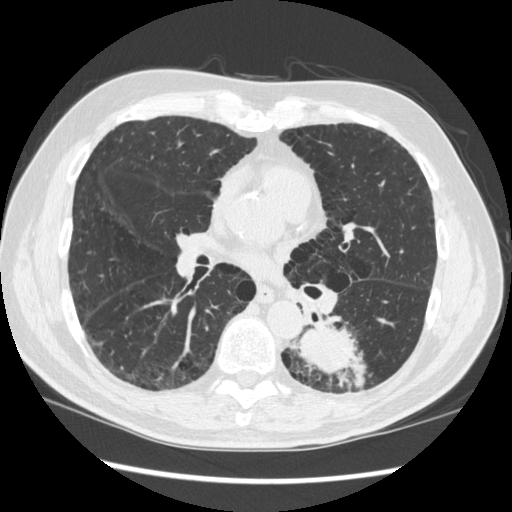
Chest CT (low-dose screening protocol), one axial image, first (baseline) screen, lung window (W 1500 / L -600 HU), 1.25 mm slice thickness, standard (soft-tissue) reconstruction kernel (STANDARD), 512 × 512 image matrix, field of view 360 × 360 mm. Male, age 72 years at enrolment.
• Expert reader's lesion annotation, bounding box (x1, y1, x2, y2) in pixels: (265, 305, 369, 398).
• The screening reader recorded 2 non-calcified nodules or masses ≥4 mm on this exam (left lower lobe, right middle lobe); which of them this box marks is not recorded.
• Official screen result: positive, change unspecified: nodule(s) >= 4 mm or enlarging nodule(s), mass(es), or other non-specific abnormalities suspicious for lung cancer.
• Lung cancer was diagnosed 37 days after this screen: squamous cell carcinoma, NOS, left lower lobe, stage IIIA (AJCC 6th edition), 60 mm at pathology.